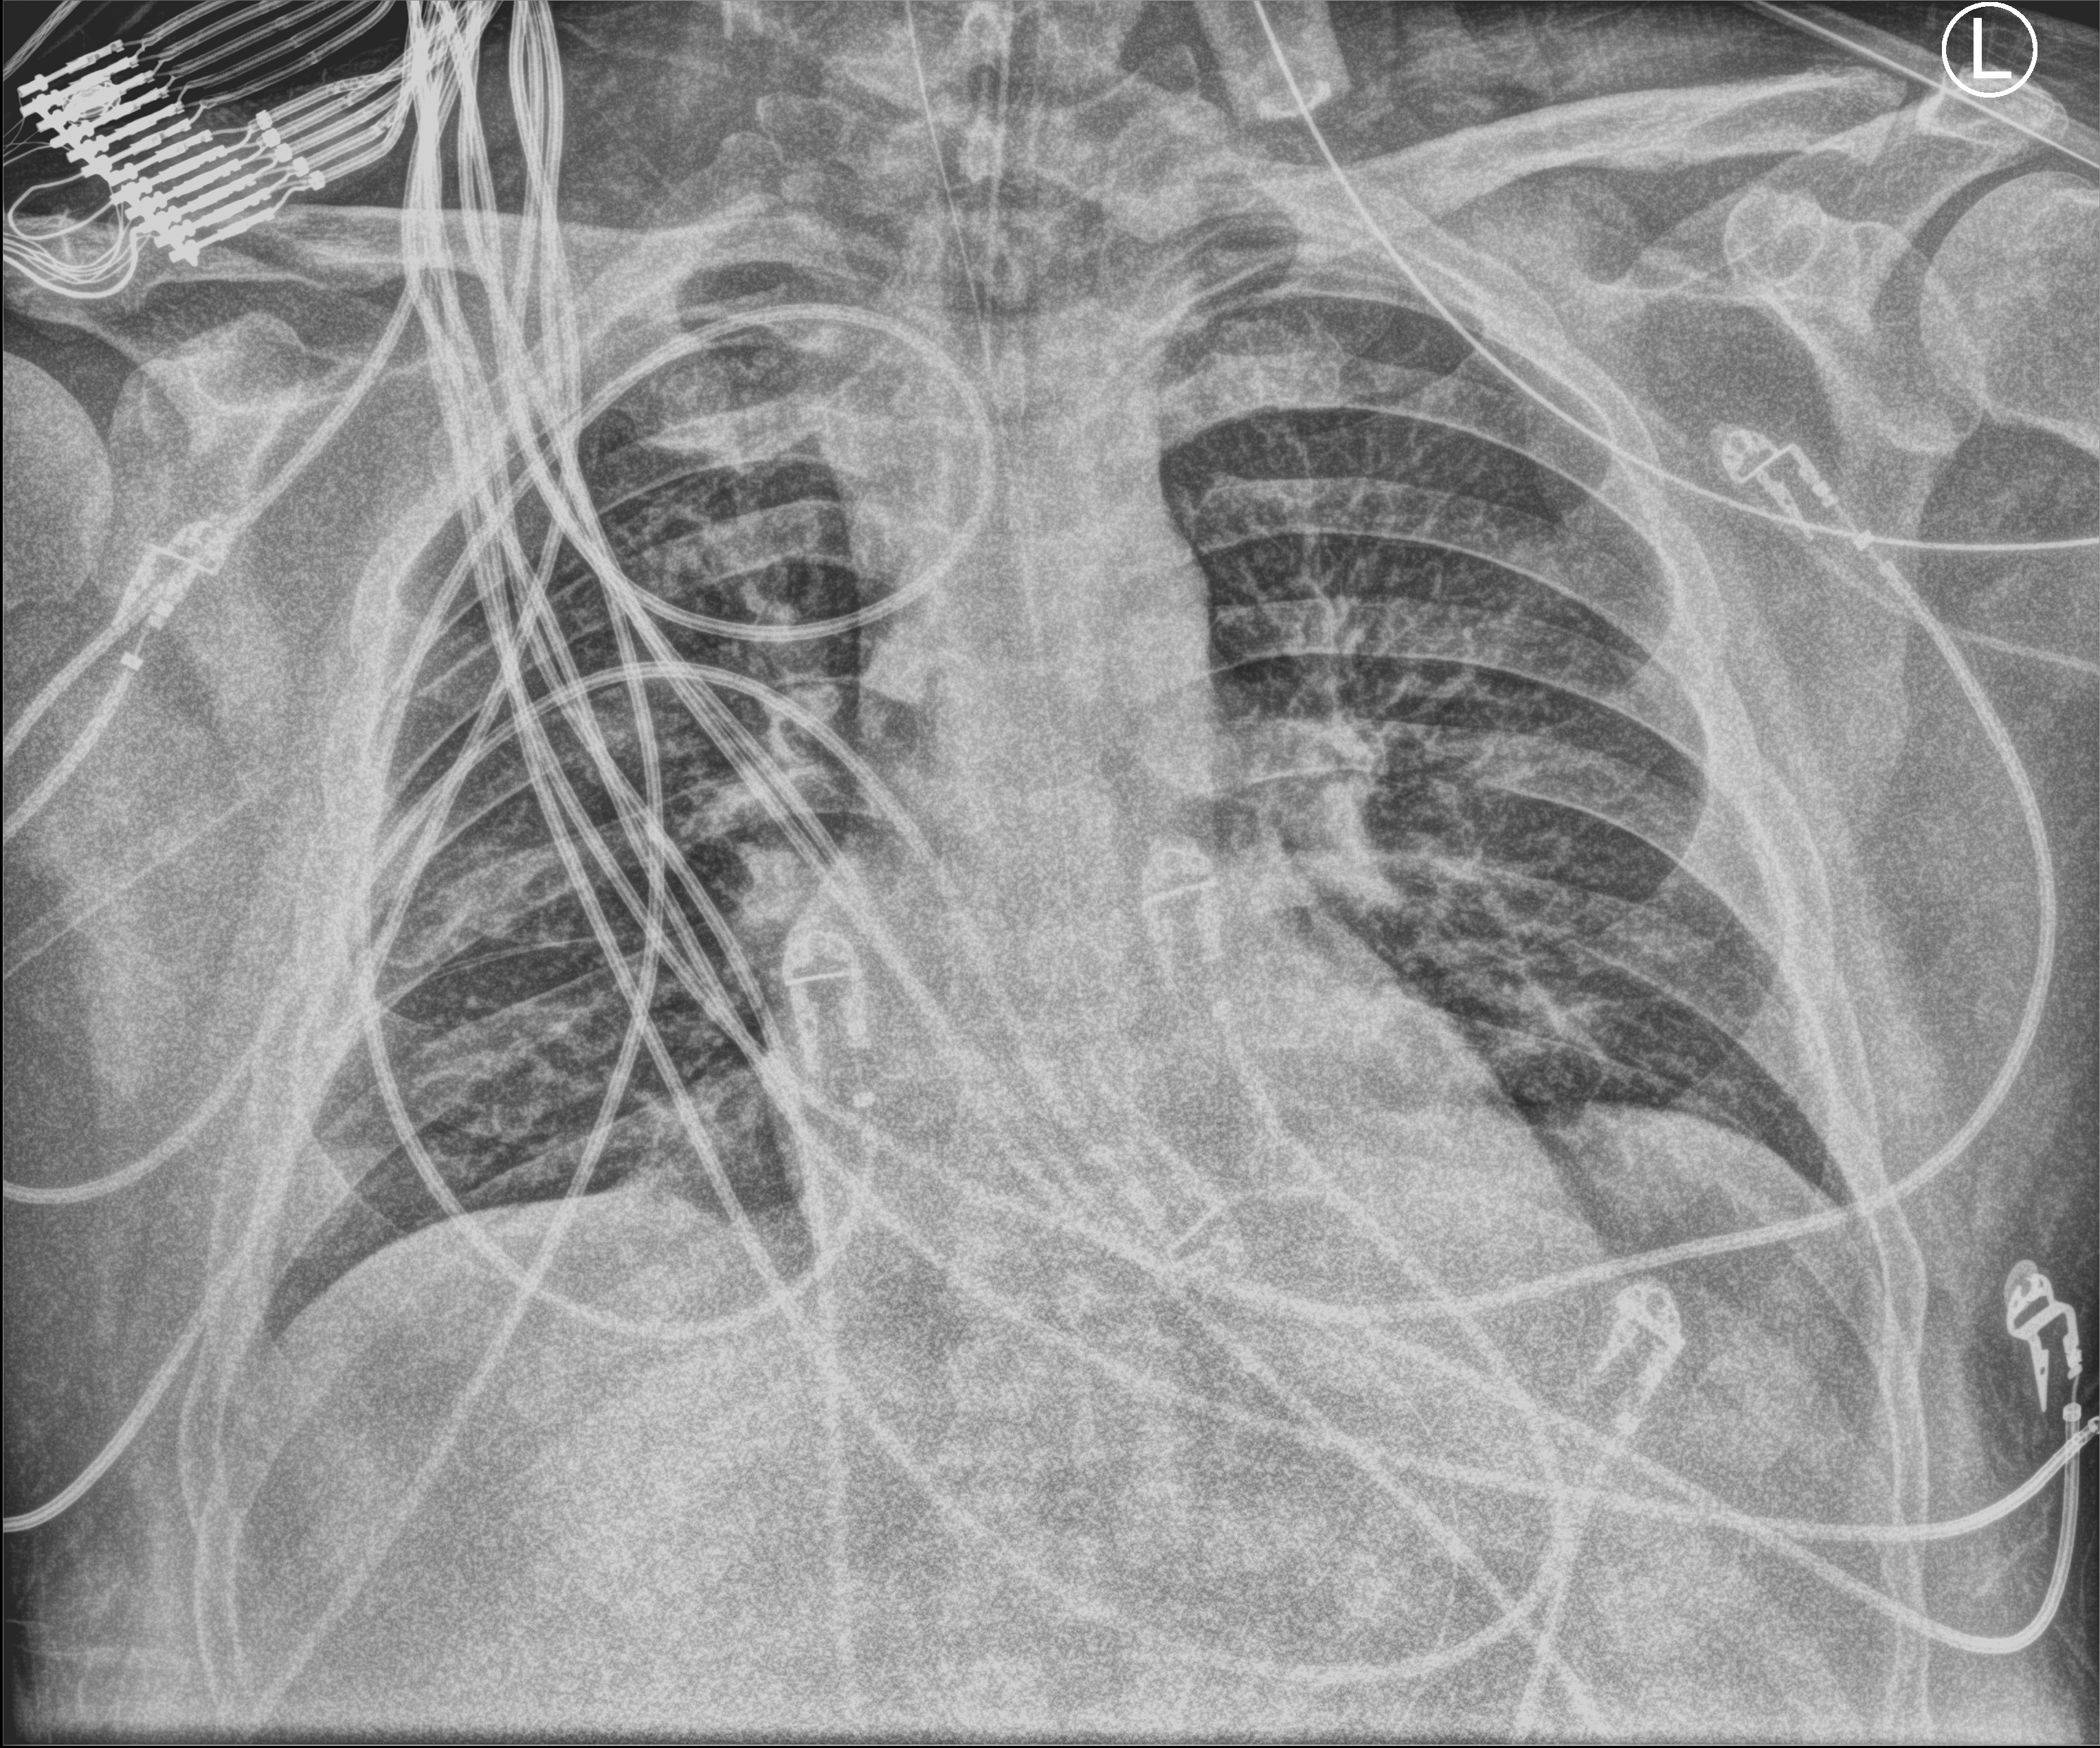
Chest X-ray (portable), anteroposterior (AP) projection. Patient hospitalised with COVID-19; male, aged 18–59 years.
Hospital-stay facts (about this admission, not read from this image; timing relative to this image not recorded): admitted to intensive care during this hospital stay: yes; mechanically ventilated during this hospital stay: yes.